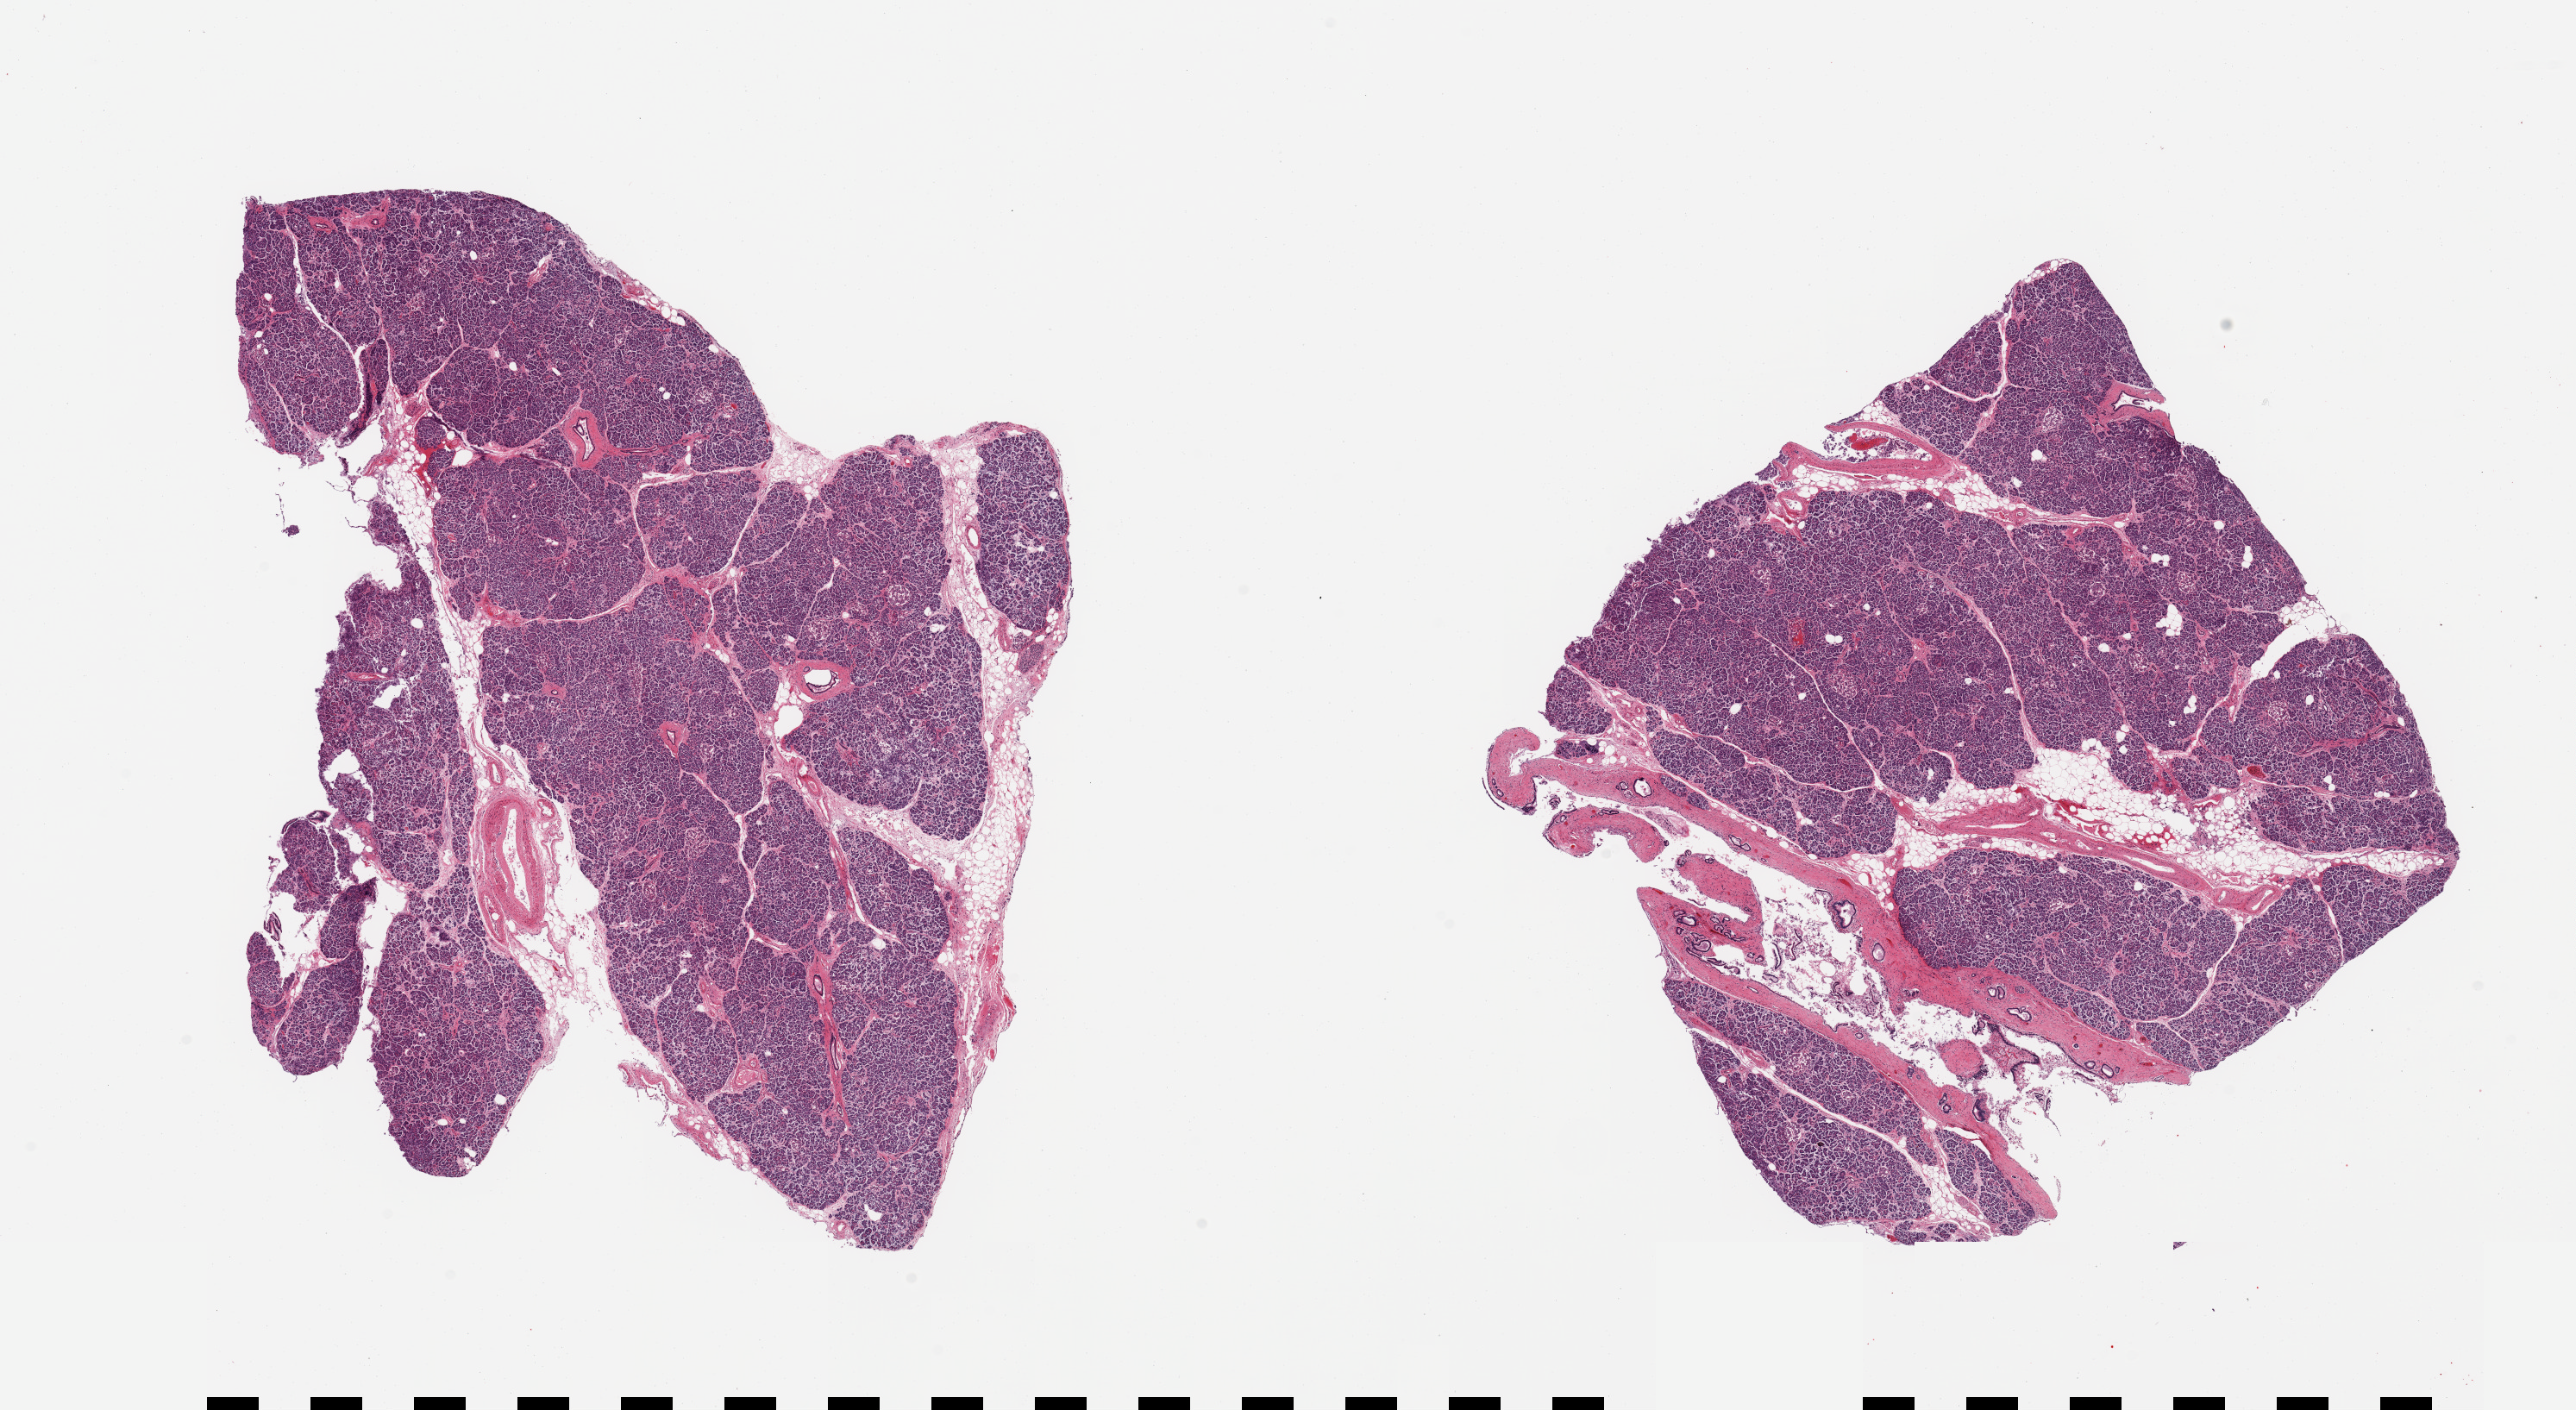
H&E whole-slide image, low-resolution overview of the scanned area, about 23.6 x 12.9 mm (slide scanned at 20x), PAXgene-fixed, paraffin-embedded tissue, target tissue: pancreas, donor tissue sample. Donor sex: male.
- pathologist's review note for this sample: 2 pieces; 10% internal fat